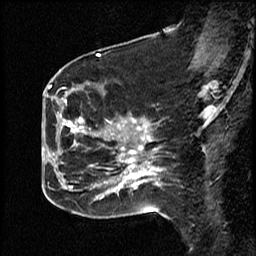
Breast MRI (dynamic contrast-enhanced), one sagittal slice. Slice 21 of 50 in the series (ordered by position). Dynamic contrast-enhanced study with each time point stored as its own series, time point 2 of 4 at this slice position (early post-contrast, ordered by acquisition time). 1.5 T. TE 4.2 ms, TR 18.5 ms. 3 mm slice thickness. 256 × 256 image matrix, field of view 200 × 200 mm. Patient: female, 44 years. From the clinical record (not read from this slice): setting: breast cancer imaged before/during neoadjuvant chemotherapy; receptor status: HR-positive, HER2-negative.
Structures marked on this image (semi-automatic segmentation, software-assisted and operator-edited):
- analysis volume of interest (the breast-tissue region the enhancement analysis was run in; not a lesion): bounding box <59,85,114,206> (left, top, right, bottom; pixels)
- tumour enhancement mask (voxels above the 100 % enhancement threshold inside the analysis volume of interest): <64,99,84,188>